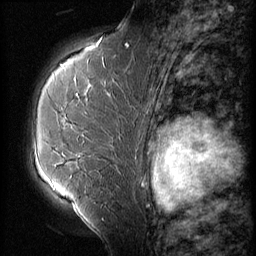
Breast MRI (dynamic contrast-enhanced), one sagittal slice. Position 40 of 56 along the scan axis. 3 images stored at this slice position (order not interpretable as contrast timing). 1.5 T. TE 4.2 ms, TR 9 ms. 2.5 mm slice thickness. 256 × 256 image matrix, field of view 180 × 180 mm. Patient: female, 51 years. Case-level facts recorded for this patient, not image findings: setting: breast cancer imaged before/during neoadjuvant chemotherapy; receptor status: HR-positive, HER2-negative.
Annotated regions visible in this slice (semi-automatic segmentation, software-assisted and operator-edited):
- analysis volume of interest (the breast-tissue region the enhancement analysis was run in; not a lesion): box from (x=24, y=56) to (x=140, y=165) px
- tumour enhancement mask (voxels above the 140 % enhancement threshold inside the analysis volume of interest): (x=76, y=86)–(x=90, y=97)